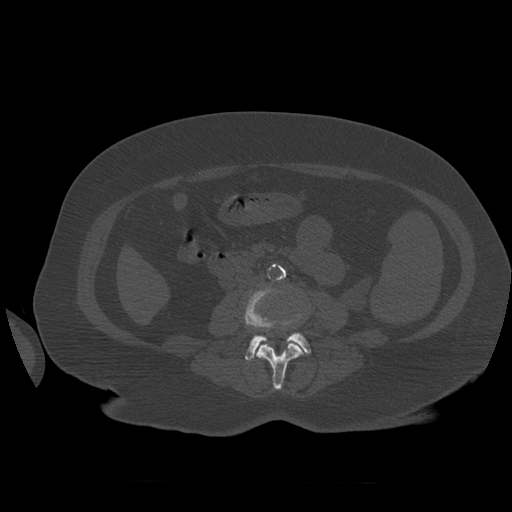
CT including the spine, one axial slice; position 218 of 399 along the scan axis; reconstruction kernel STANDARD; bone window (W 1800 / L 400 HU); 1.25 mm slice thickness; 512 × 512 image matrix. Patient age 81 years. From the clinical record (not read from this slice): primary cancer: renal.
Annotated regions visible in this slice (semi-automatically segmented with operator editing):
- L3 vertebra: bounding box <255,343,304,390> (left, top, right, bottom; pixels)
- L4 vertebra: <245,289,311,361>